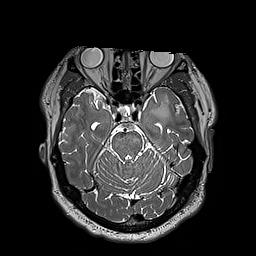
Brain MRI from a brain-tumour surgery series, one axial slice; 1 mm slice thickness; 256 × 256 image matrix. Case-level facts recorded for this patient, not image findings: histopathology: Astrocytoma; WHO grade: 3; IDH mutation: yes.
Annotated regions visible in this slice (expert manual segmentation):
- tumour: bounding box [x1, y1, x2, y2] px = [151, 96, 169, 122]